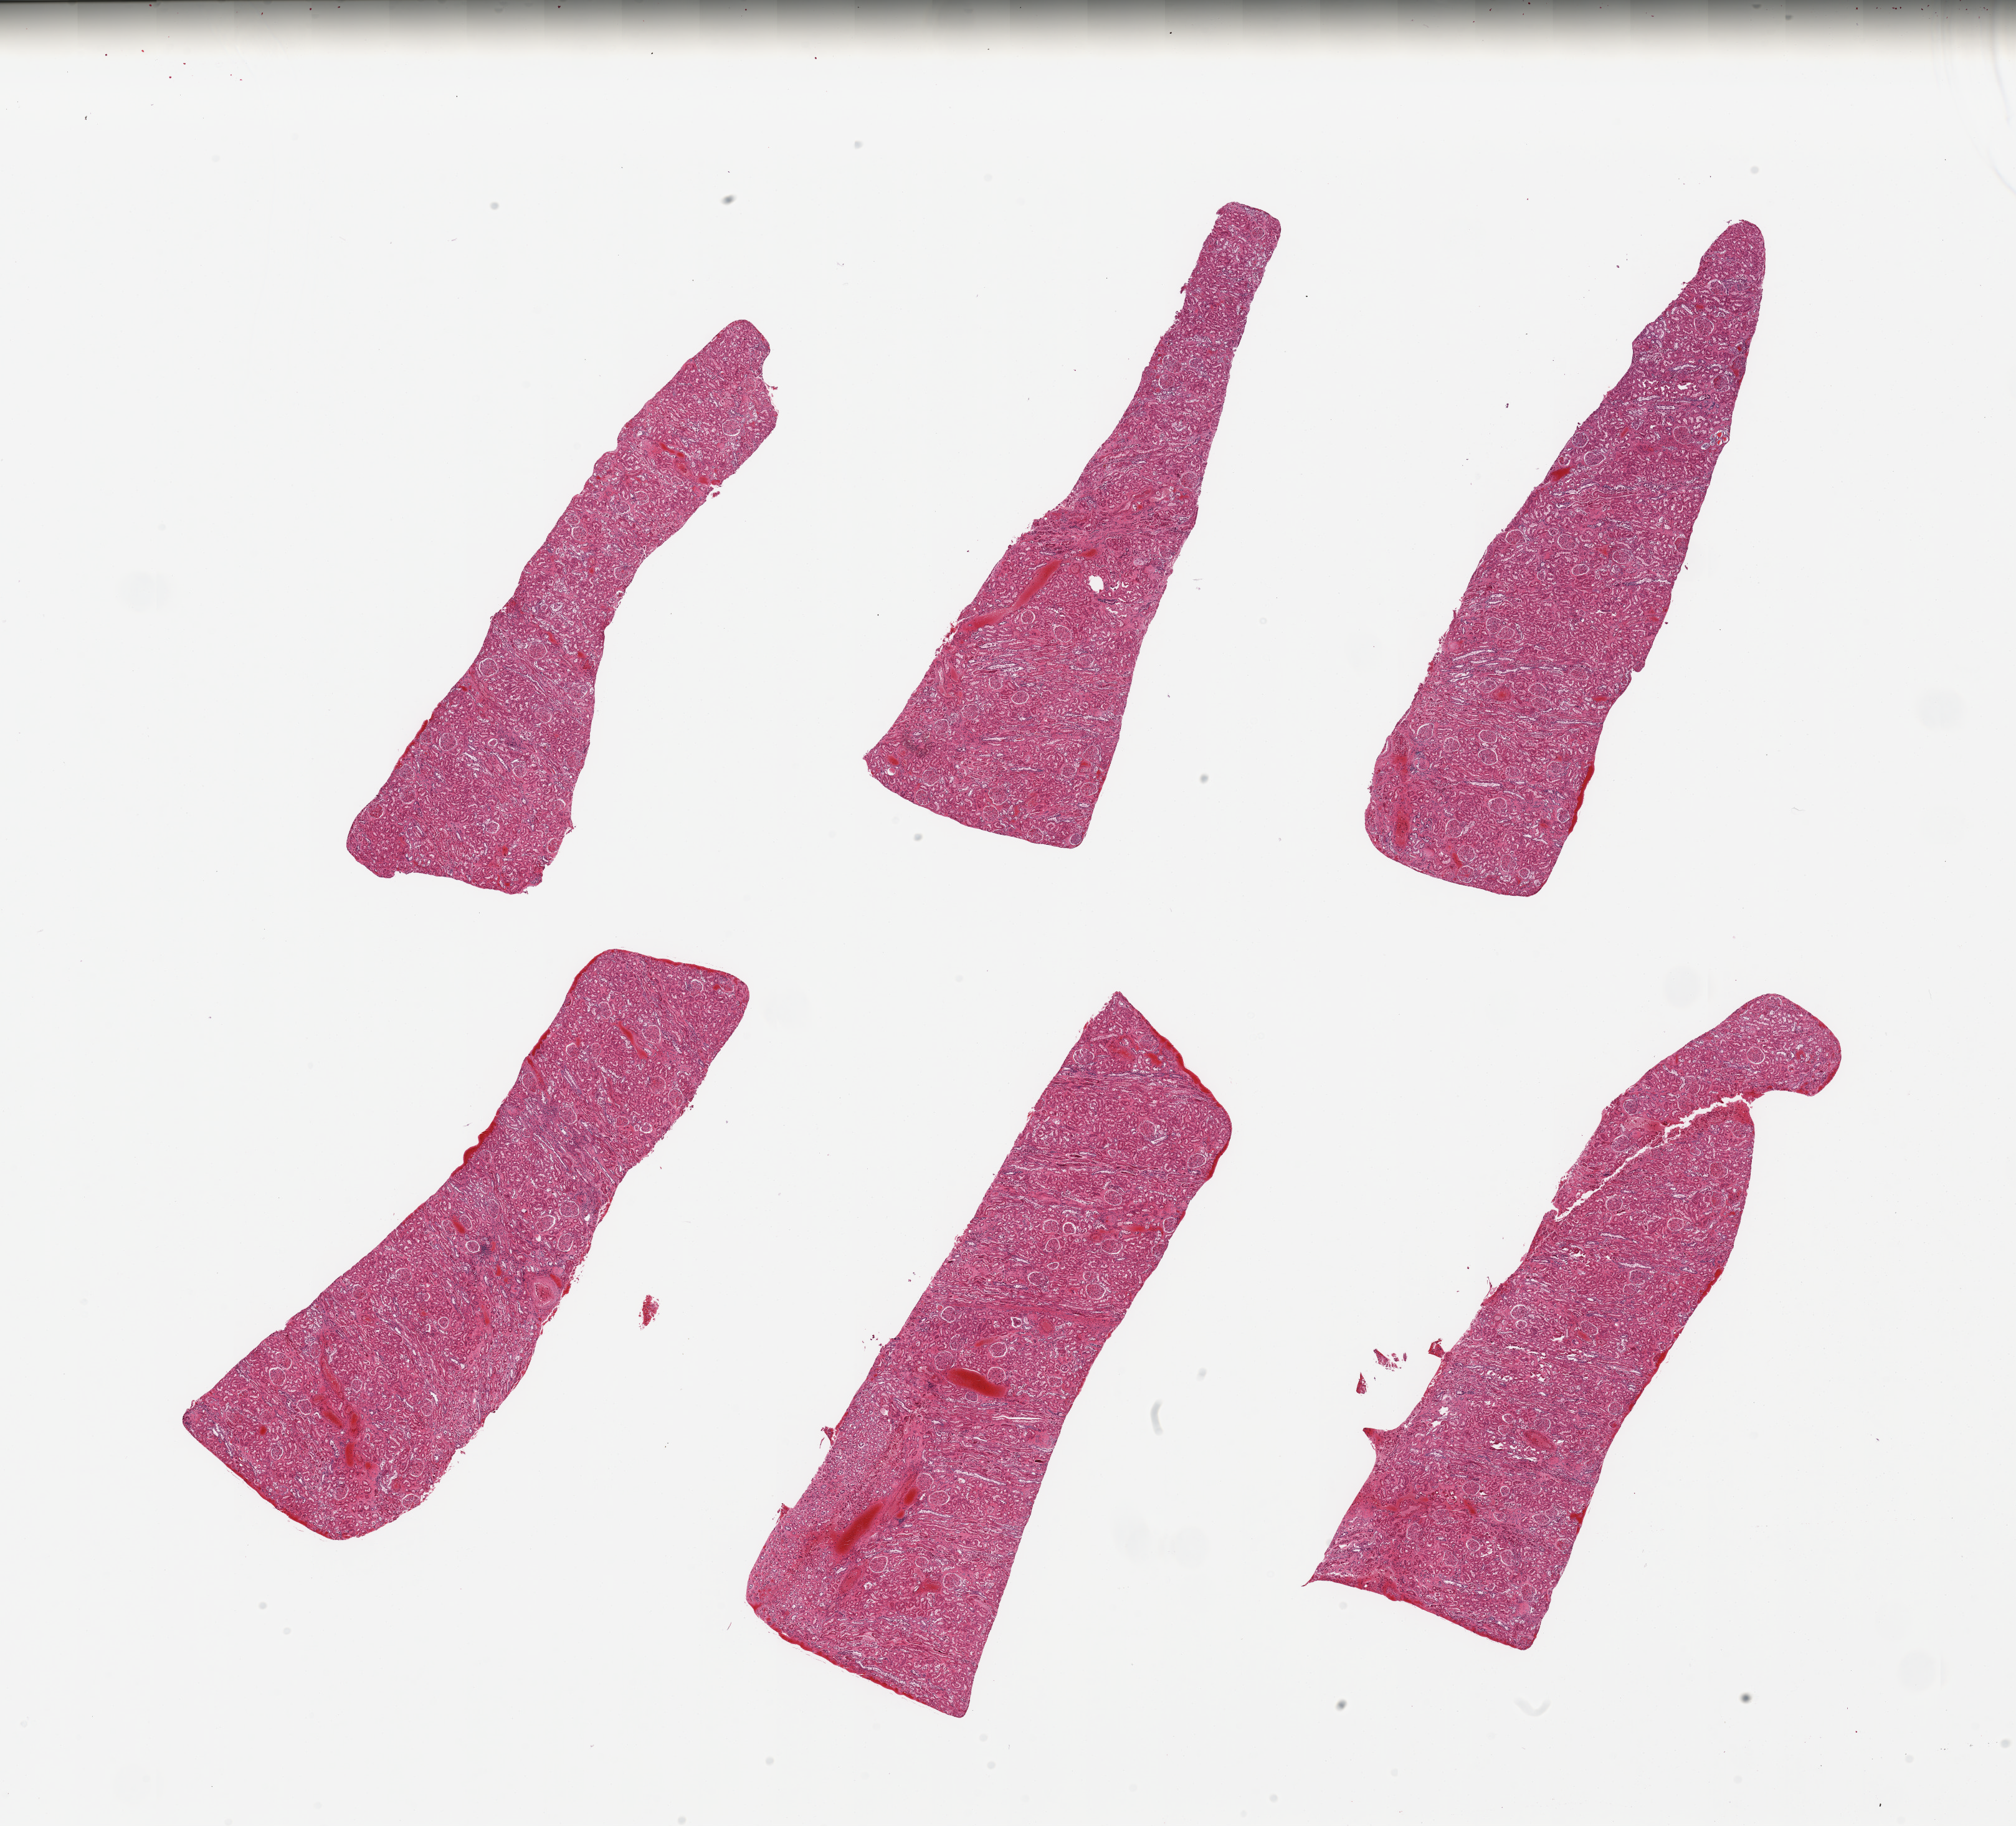
Whole-slide image, hematoxylin and eosin (H&E) stain, brightfield — whole scanned area (about 25.6 x 23.2 mm) shown as a low-resolution overview, PAXgene-fixed, paraffin-embedded tissue, section of renal cortex (target tissue), donor tissue sample. Donor: male.
Pathologist's review note for this sample: 6 pieces; glomeruli in all sections, few sclerotic glomeruli, small portion of medulla.